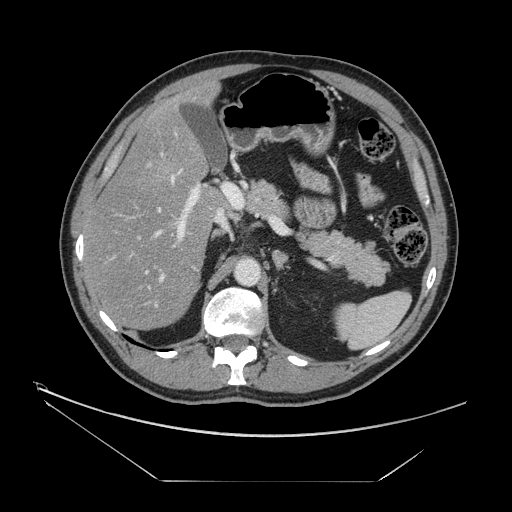
Contrast-enhanced abdominal CT, one axial slice. Position 85 of 161 along the scan axis. Intravenous contrast given. Soft-tissue window (W 400 / L 40 HU). 2.5 mm slice thickness. 512 × 512 image matrix. Male patient, age 65 years. Case-level facts recorded for this patient, not image findings: diagnosis: colorectal cancer liver metastases, imaged before liver resection; multiple liver metastases: yes.
Annotated regions visible in this slice (expert manual segmentation):
- hepatic veins: bounding box [x1, y1, x2, y2] px = [137, 168, 183, 290]
- liver: [85, 86, 223, 329]
- planned liver remnant (the part of the liver to remain after resection): [92, 86, 222, 329]
- portal vein (with intrahepatic branches): [112, 153, 220, 309]